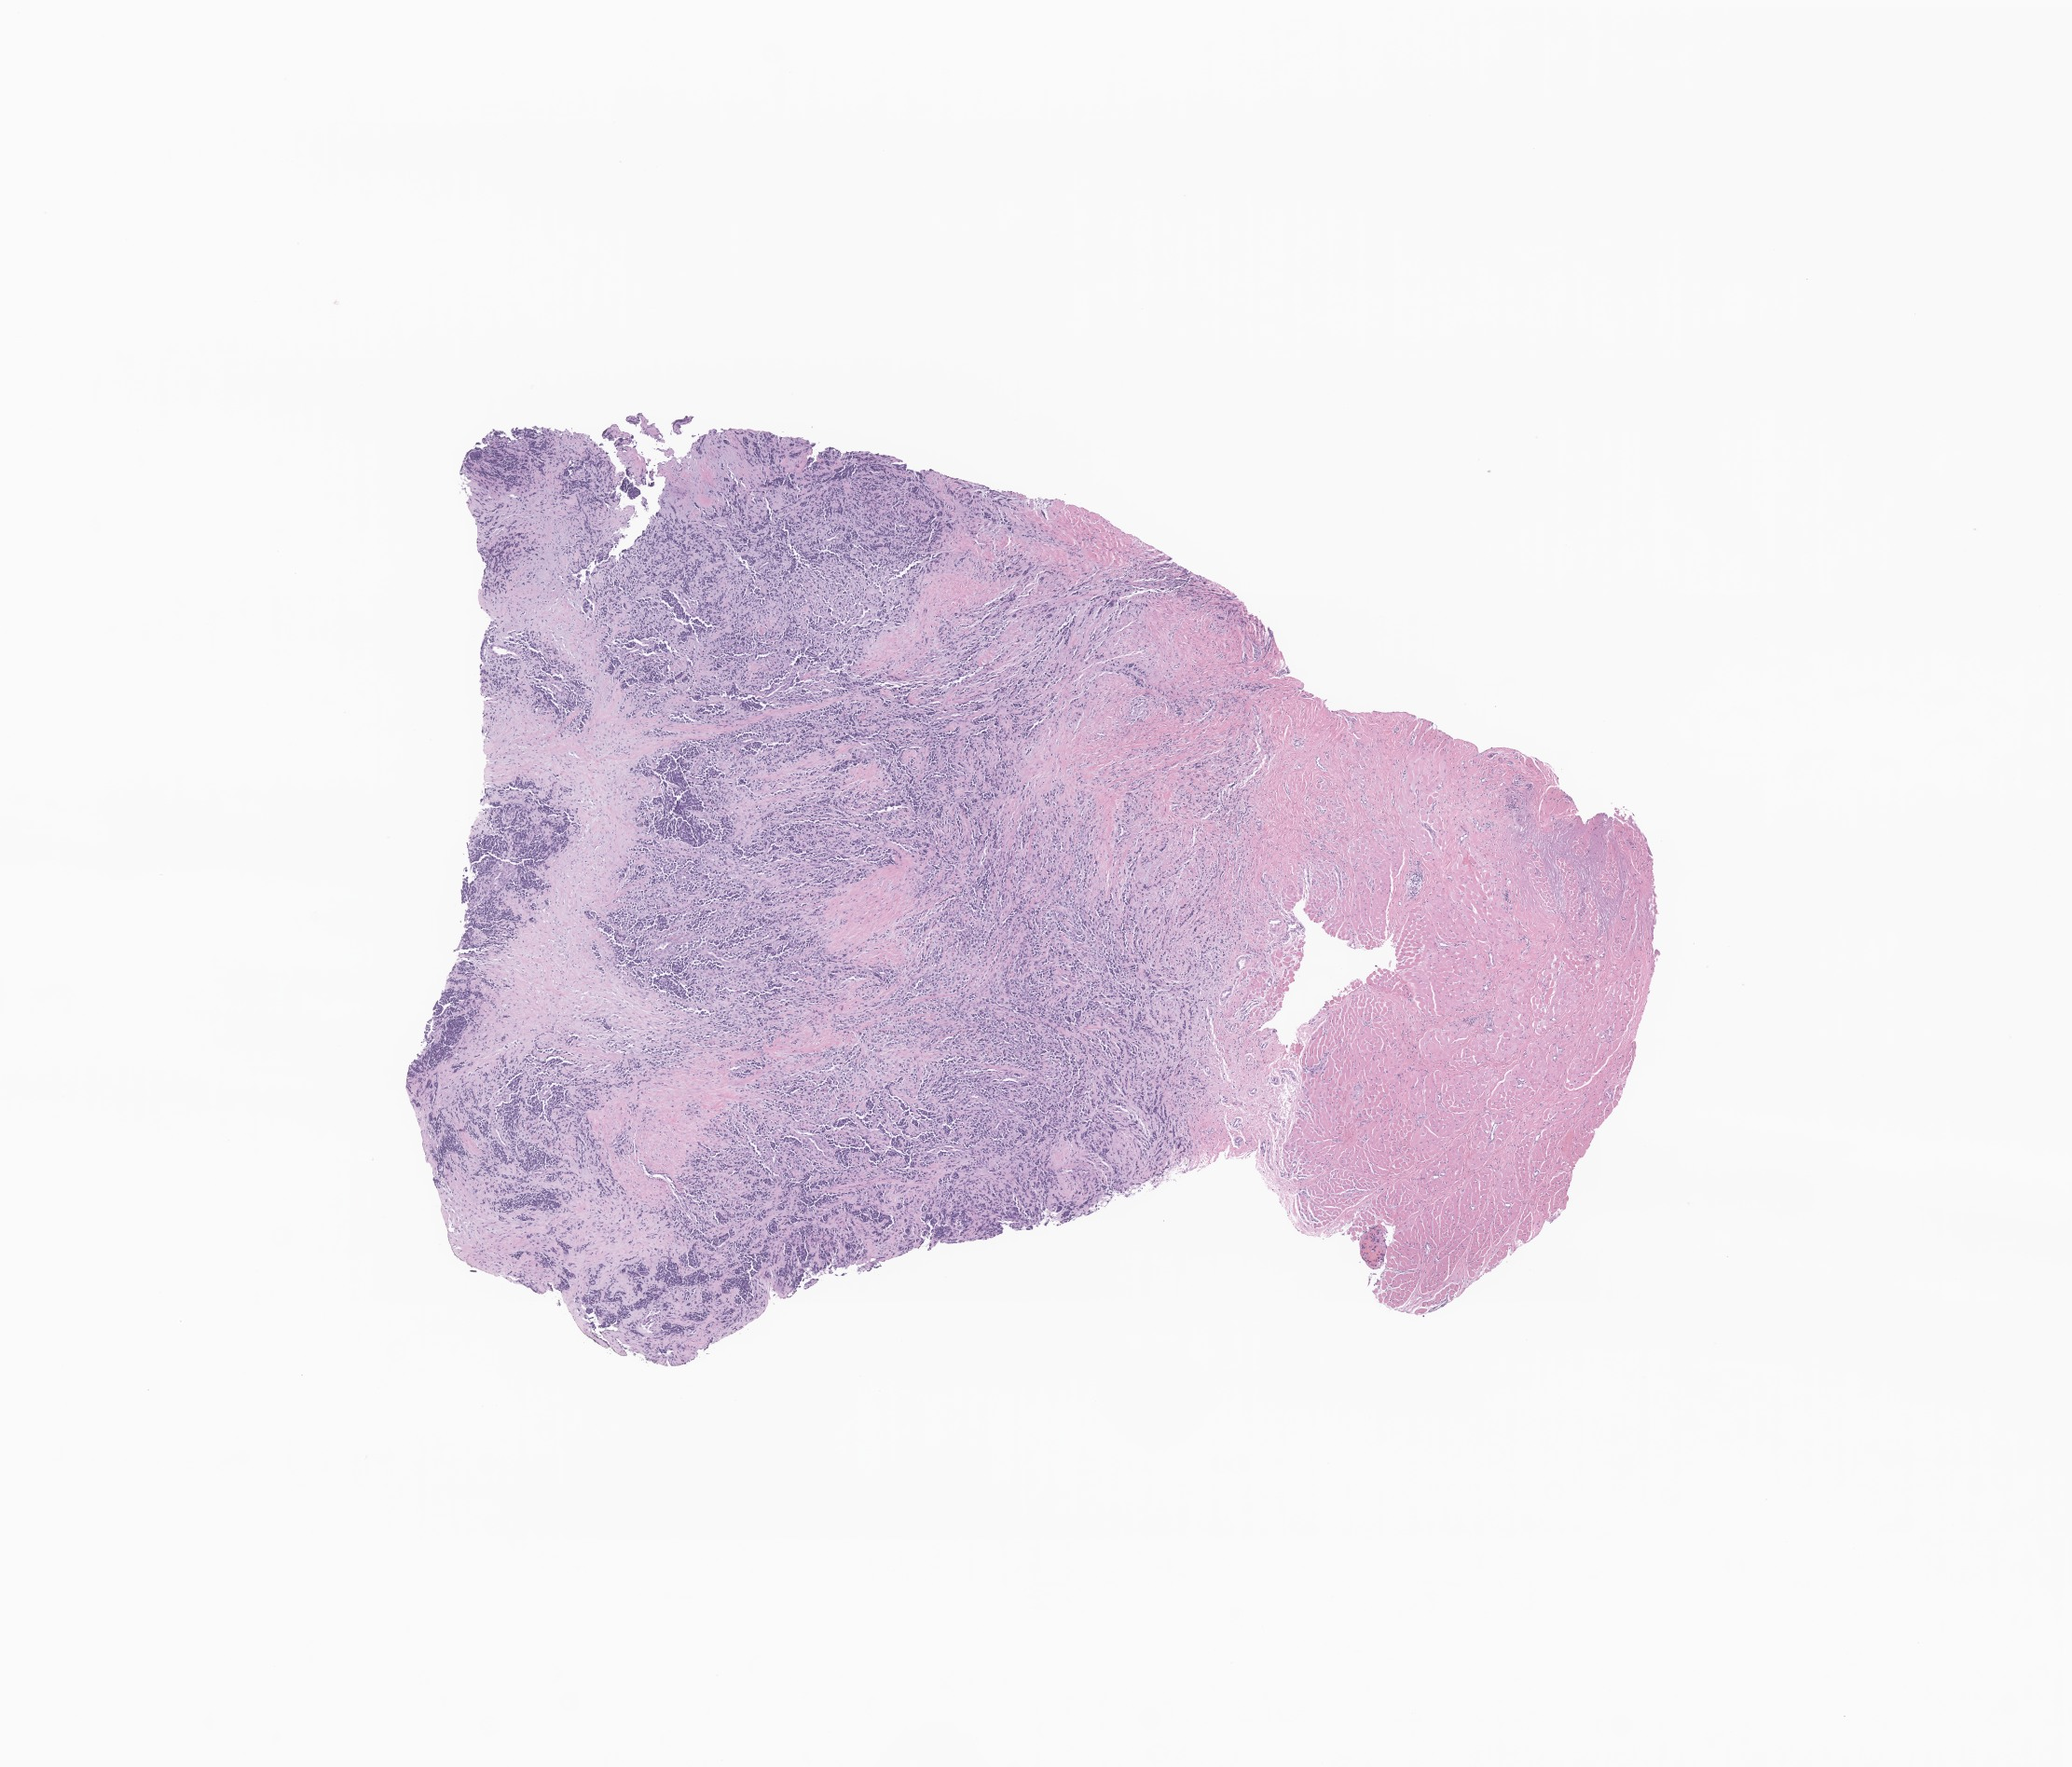
H&E whole-slide image of tumor tissue from the soft tissues of head and neck, low-resolution overview of the scanned area, about 9.4 x 8.0 mm, formalin-fixed, paraffin-embedded (FFPE) tissue. Patient female; age 50 months (4 years 2 months).
Recorded diagnosis: Rhabdomyosarcoma, NOS.